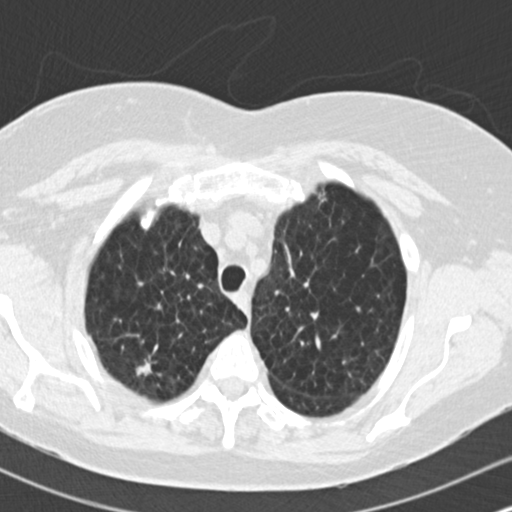
Axial slice from a low-dose chest CT screening exam. Baseline screening round. Lung window (W 1500 / L -600 HU). 2 mm slice thickness. Slice 32 of 172 in the series. Female, age 73 years at enrolment. Former smoker at enrolment.
Lesion marked by an expert reader, box from (x=119, y=333) to (x=174, y=389) px. The screening reader recorded 2 non-calcified nodules or masses ≥4 mm on this exam; which of them this box marks is not recorded. Lung cancer was diagnosed 601 days after this screen: adenocarcinoma, NOS, right upper lobe, moderately differentiated (G2), stage IB (AJCC 6th edition), 15 mm at pathology.